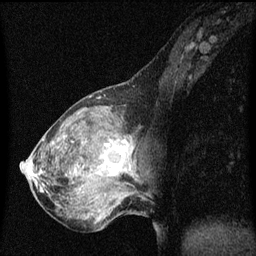
Breast MRI (dynamic contrast-enhanced), one sagittal slice; slice 23 of 60 in the series (ordered by position); dynamic contrast-enhanced series, image 2 of 3 at this slice position (ordered by acquisition); 1.5 T; TE 4.2 ms, TR 8 ms; 2 mm slice thickness; 256 × 256 image matrix. Female patient, age 50 years.
Outlined on this slice (semi-automatically segmented with operator editing):
- analysis volume of interest (the breast-tissue region the enhancement analysis was run in; not a lesion): bounding box <91,126,138,189> (left, top, right, bottom; pixels)
- tumour enhancement mask (voxels above the 70 % enhancement threshold inside the analysis volume of interest): <102,140,127,175>